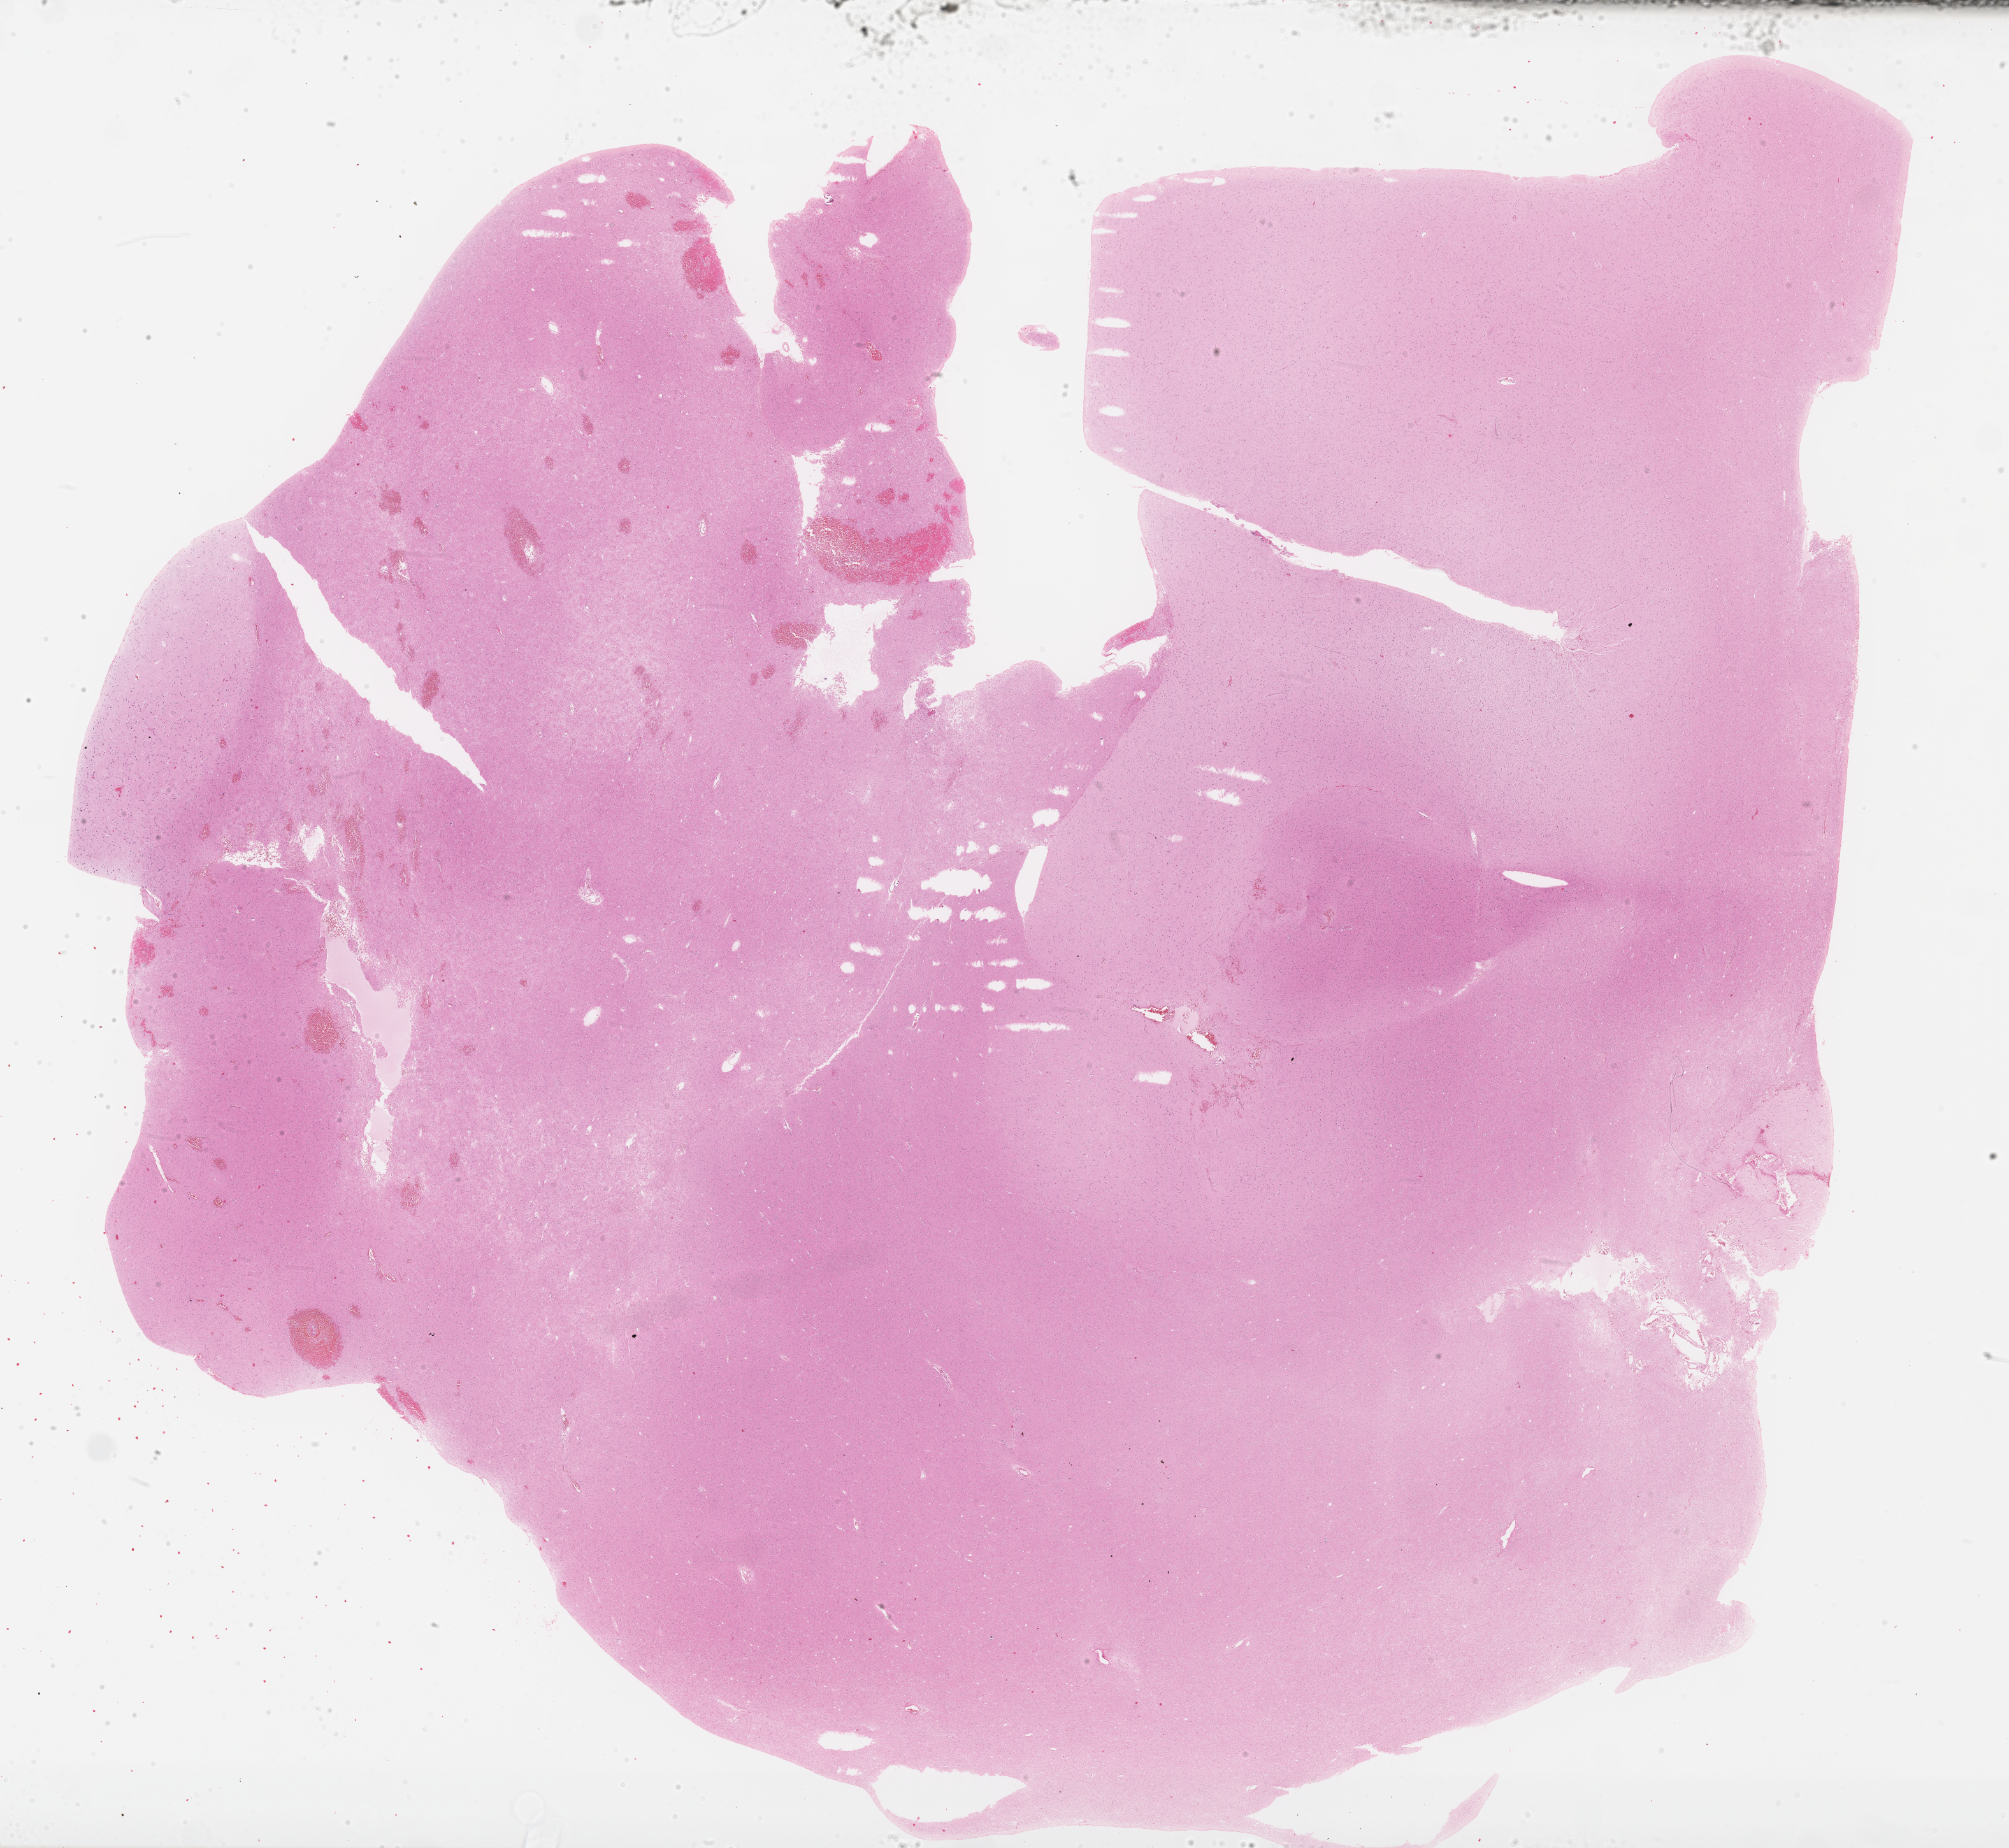
Digitized H&E tissue section (whole slide) — shown as a low-resolution overview of the whole scanned area (about 25.4 x 23.4 mm, from a 40x scan), formalin-fixed paraffin-embedded (FFPE) diagnostic section, primary tumour sample from the brain. Patient: male, age at initial diagnosis 40 years. Histologic grade: G2 (moderately differentiated).
* diagnosis: Oligodendroglioma, NOS (cerebrum)